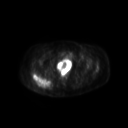
FDG PET of an extremity soft-tissue mass (from a PET/CT study), one axial slice; slice 49 of 267 in the series (ordered by position); 128 × 128 image matrix, field of view 600 × 600 mm. Patient: female, 60 years. From the clinical record (not read from this slice): histological type: spindle cell suggestive of myxofibrosarcoma; grade: intermediate; site of the primary tumour: right buttock.
Outlined on this slice (expert contour drawn on MRI and transferred to this co-registered scan by the dataset authors):
- gross tumour volume (mass): bounding box (x1, y1, x2, y2) in pixels: (32, 73, 50, 88)